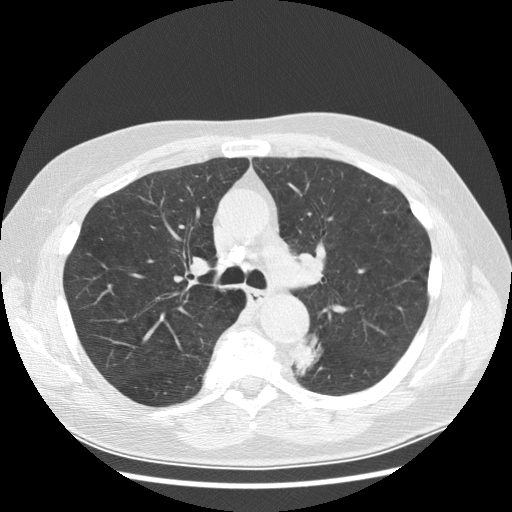
Chest CT (low-dose screening protocol), one axial image; first (baseline) screen; lung window (W 1500 / L -600 HU); 2.5 mm slice thickness; standard (soft-tissue) reconstruction kernel (STANDARD); 120 kVp; slice 95 of 282 in the series; 512 × 512 image matrix. Male, age 70 years at enrolment.
Expert reader's lesion annotation, box from (x=277, y=336) to (x=326, y=379) px. The exam's reader record, not a measurement of the box and not confirmed to be the same lesion: non-calcified nodule or mass ≥4 mm, left lower lobe, 27 × 16 mm, spiculated (stellate) margins, soft tissue attenuation, pre-existing on the prior screen: yes; interval growth: yes. Official screen result: positive, change unspecified: nodule(s) >= 4 mm or enlarging nodule(s), mass(es), or other non-specific abnormalities suspicious for lung cancer. Participant outcome: lung cancer diagnosed 97 days after this screen — papillary adenocarcinoma, NOS, left lower lobe, moderately differentiated (G2), stage IB (AJCC 6th edition), 35 mm at pathology.